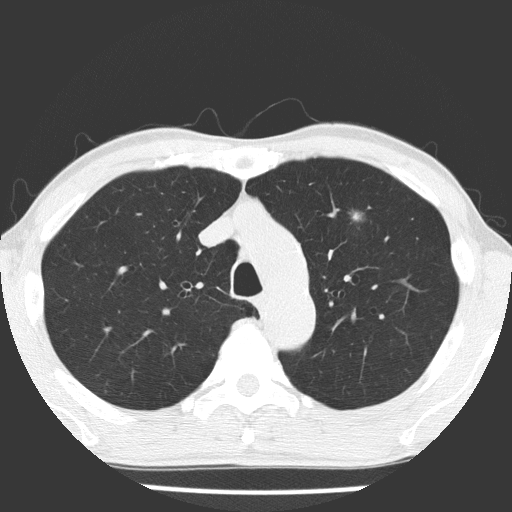
Low-dose screening chest CT, one axial slice; position 127 of 177 along the scan axis; reconstruction kernel FC51; 120 kVp; lung window (W 1500 / L -600 HU); 2 mm slice thickness; 512 × 512 image matrix.
Annotated regions visible in this slice (manually delineated by an expert):
- lesion 1 (tumor, upper lobe of left lung): box from (x=350, y=210) to (x=366, y=222) px